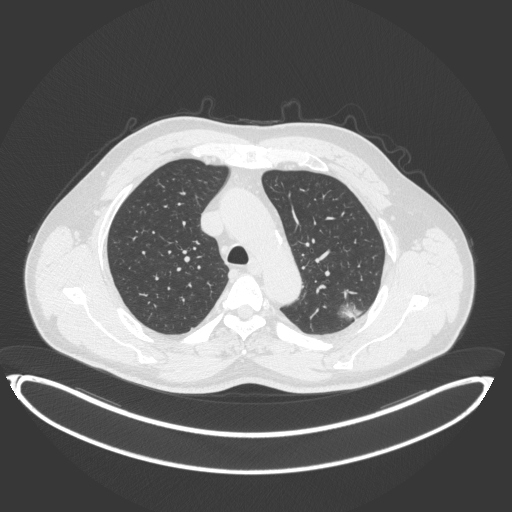
Chest CT, one axial slice; position 267 of 399 along the scan axis; lung window (W 1500 / L -600 HU); 1 mm slice thickness; 512 × 512 image matrix, field of view 469 × 469 mm. Patient: male, 58 years. From the clinical record (not read from this slice): clinical TNM (as recorded): T1c N0 M0; histopathological grade: G1-2.
Annotated regions visible in this slice (rectangle marked by the reading radiologist):
- lung tumour (recorded histology: adenocarcinoma): bounding box (x1, y1, x2, y2) in pixels: (335, 297, 365, 324)